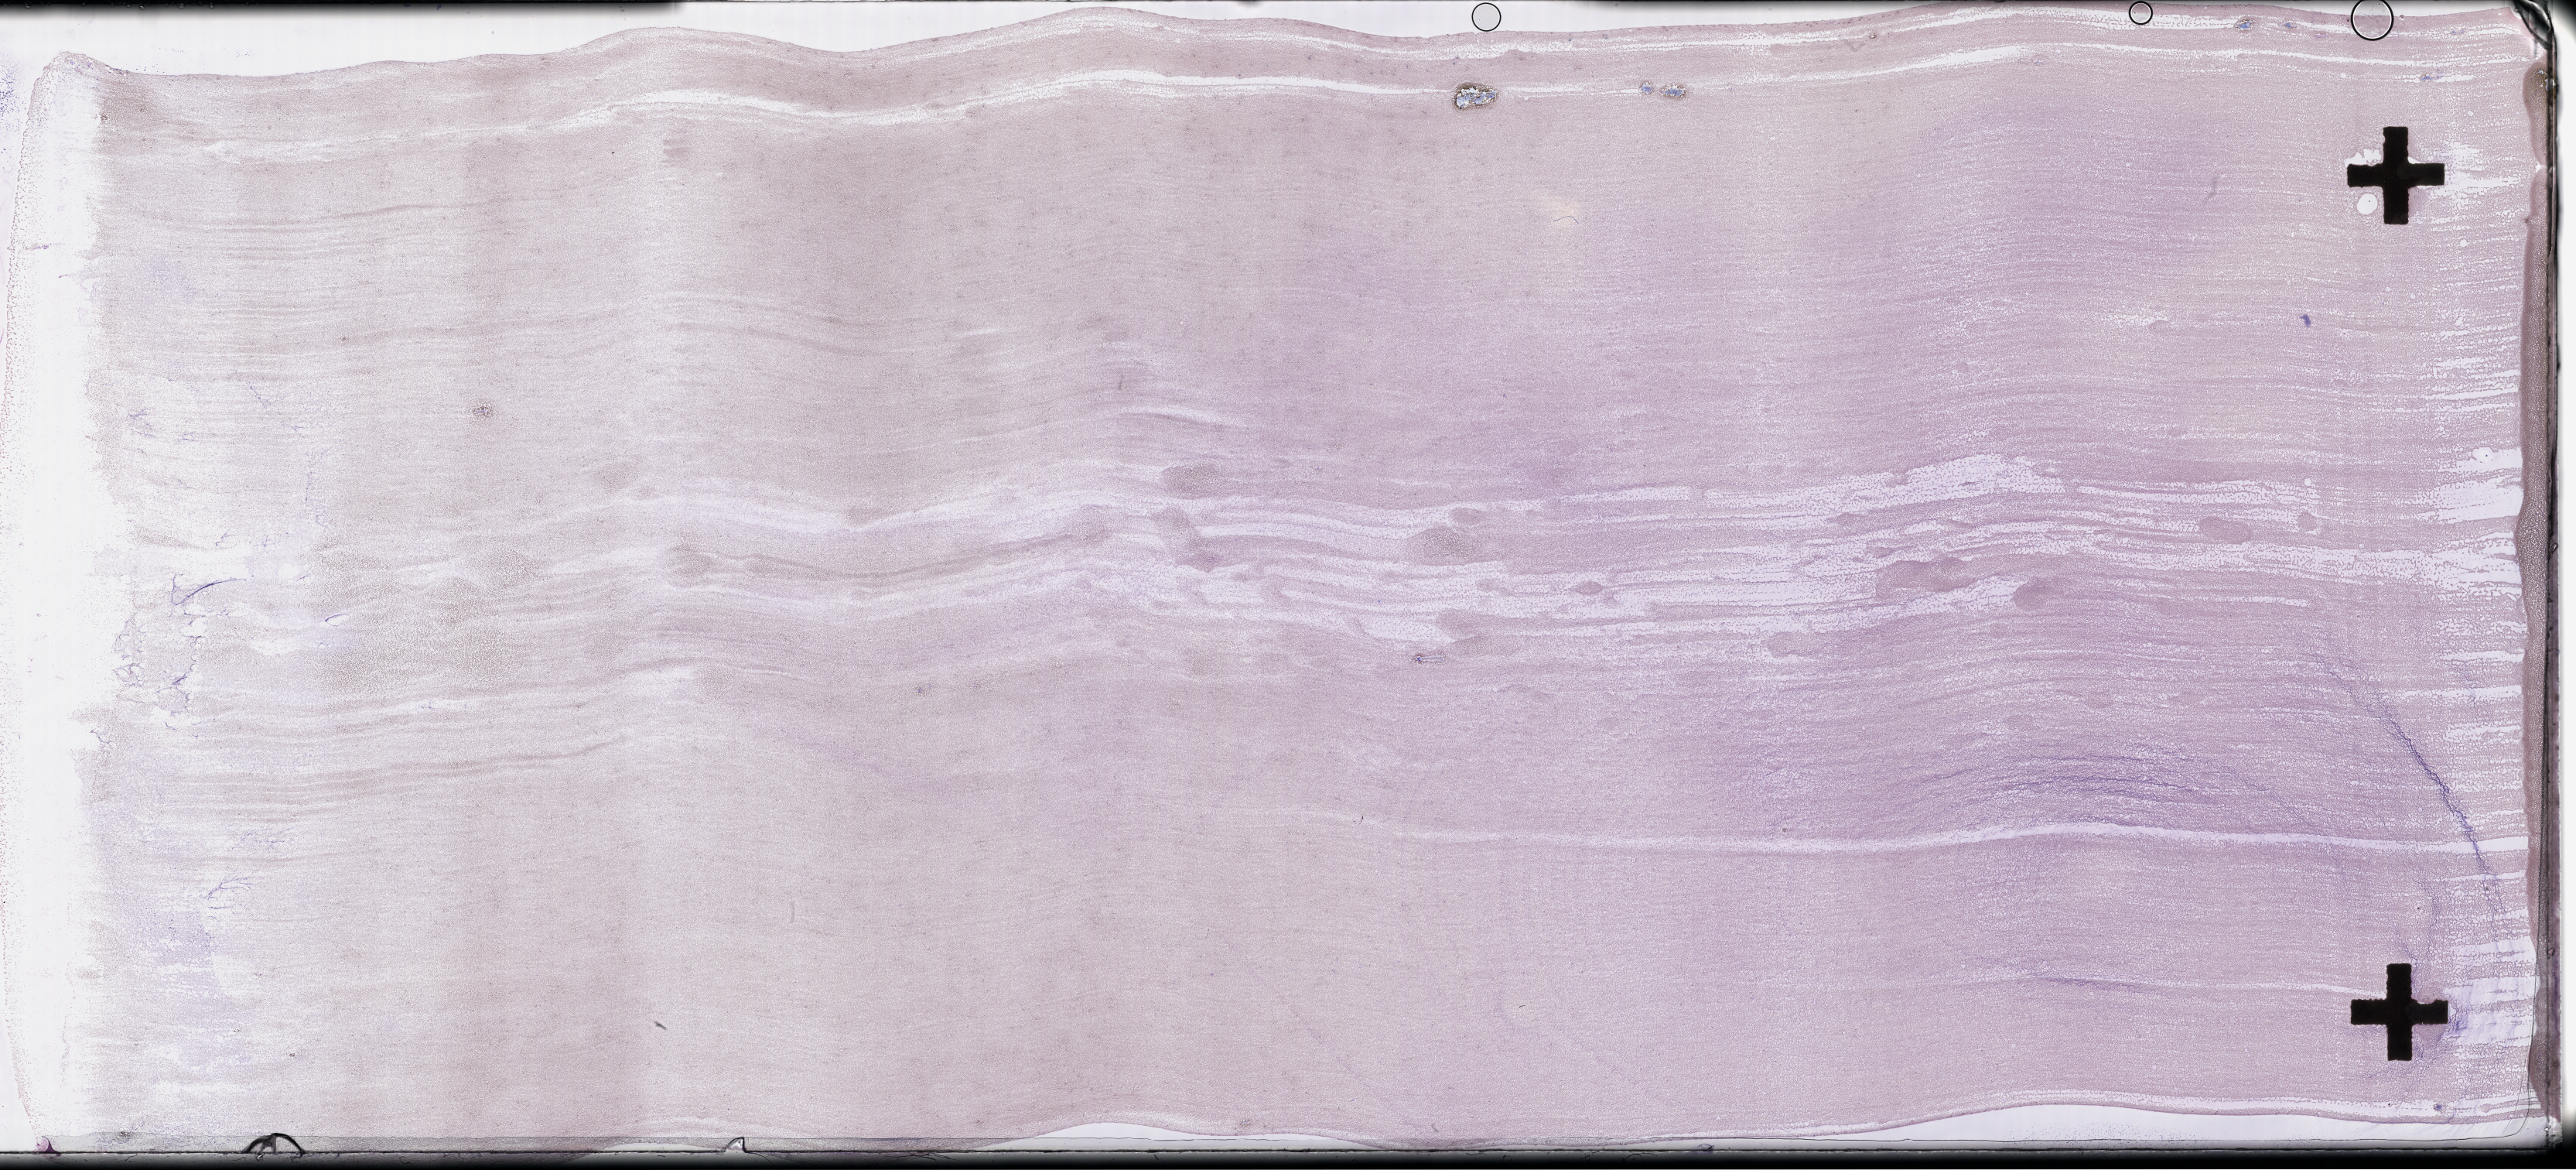
Wright–Giemsa-stained whole blood smear, whole-slide image, shown as a low-resolution overview of the whole scanned area (about 53.8 x 24.4 mm); EDTA-anticoagulated smear. Patient: male.
From a patient with: Plasma Cell Myeloma.